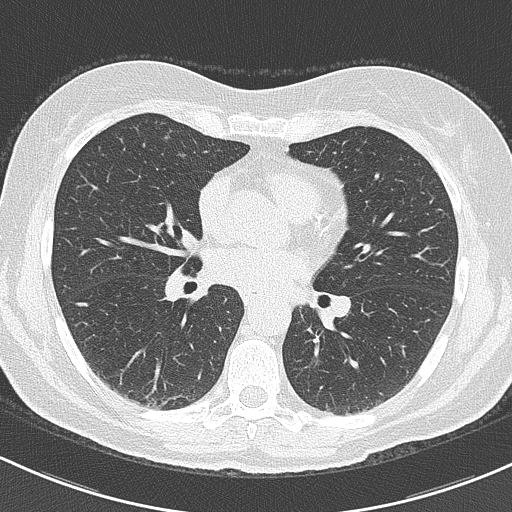
Low-dose screening chest CT, one axial slice. Position 103 of 201 along the scan axis. 120 kVp. Lung window (W 1500 / L -600 HU). 2 mm slice thickness. 512 × 512 image matrix, field of view 312 × 312 mm.
Annotated regions visible in this slice (outlined manually by an expert reader):
- lesion 1 (tumor, upper lobe of right lung): bounding box <75,302,89,307> (left, top, right, bottom; pixels)